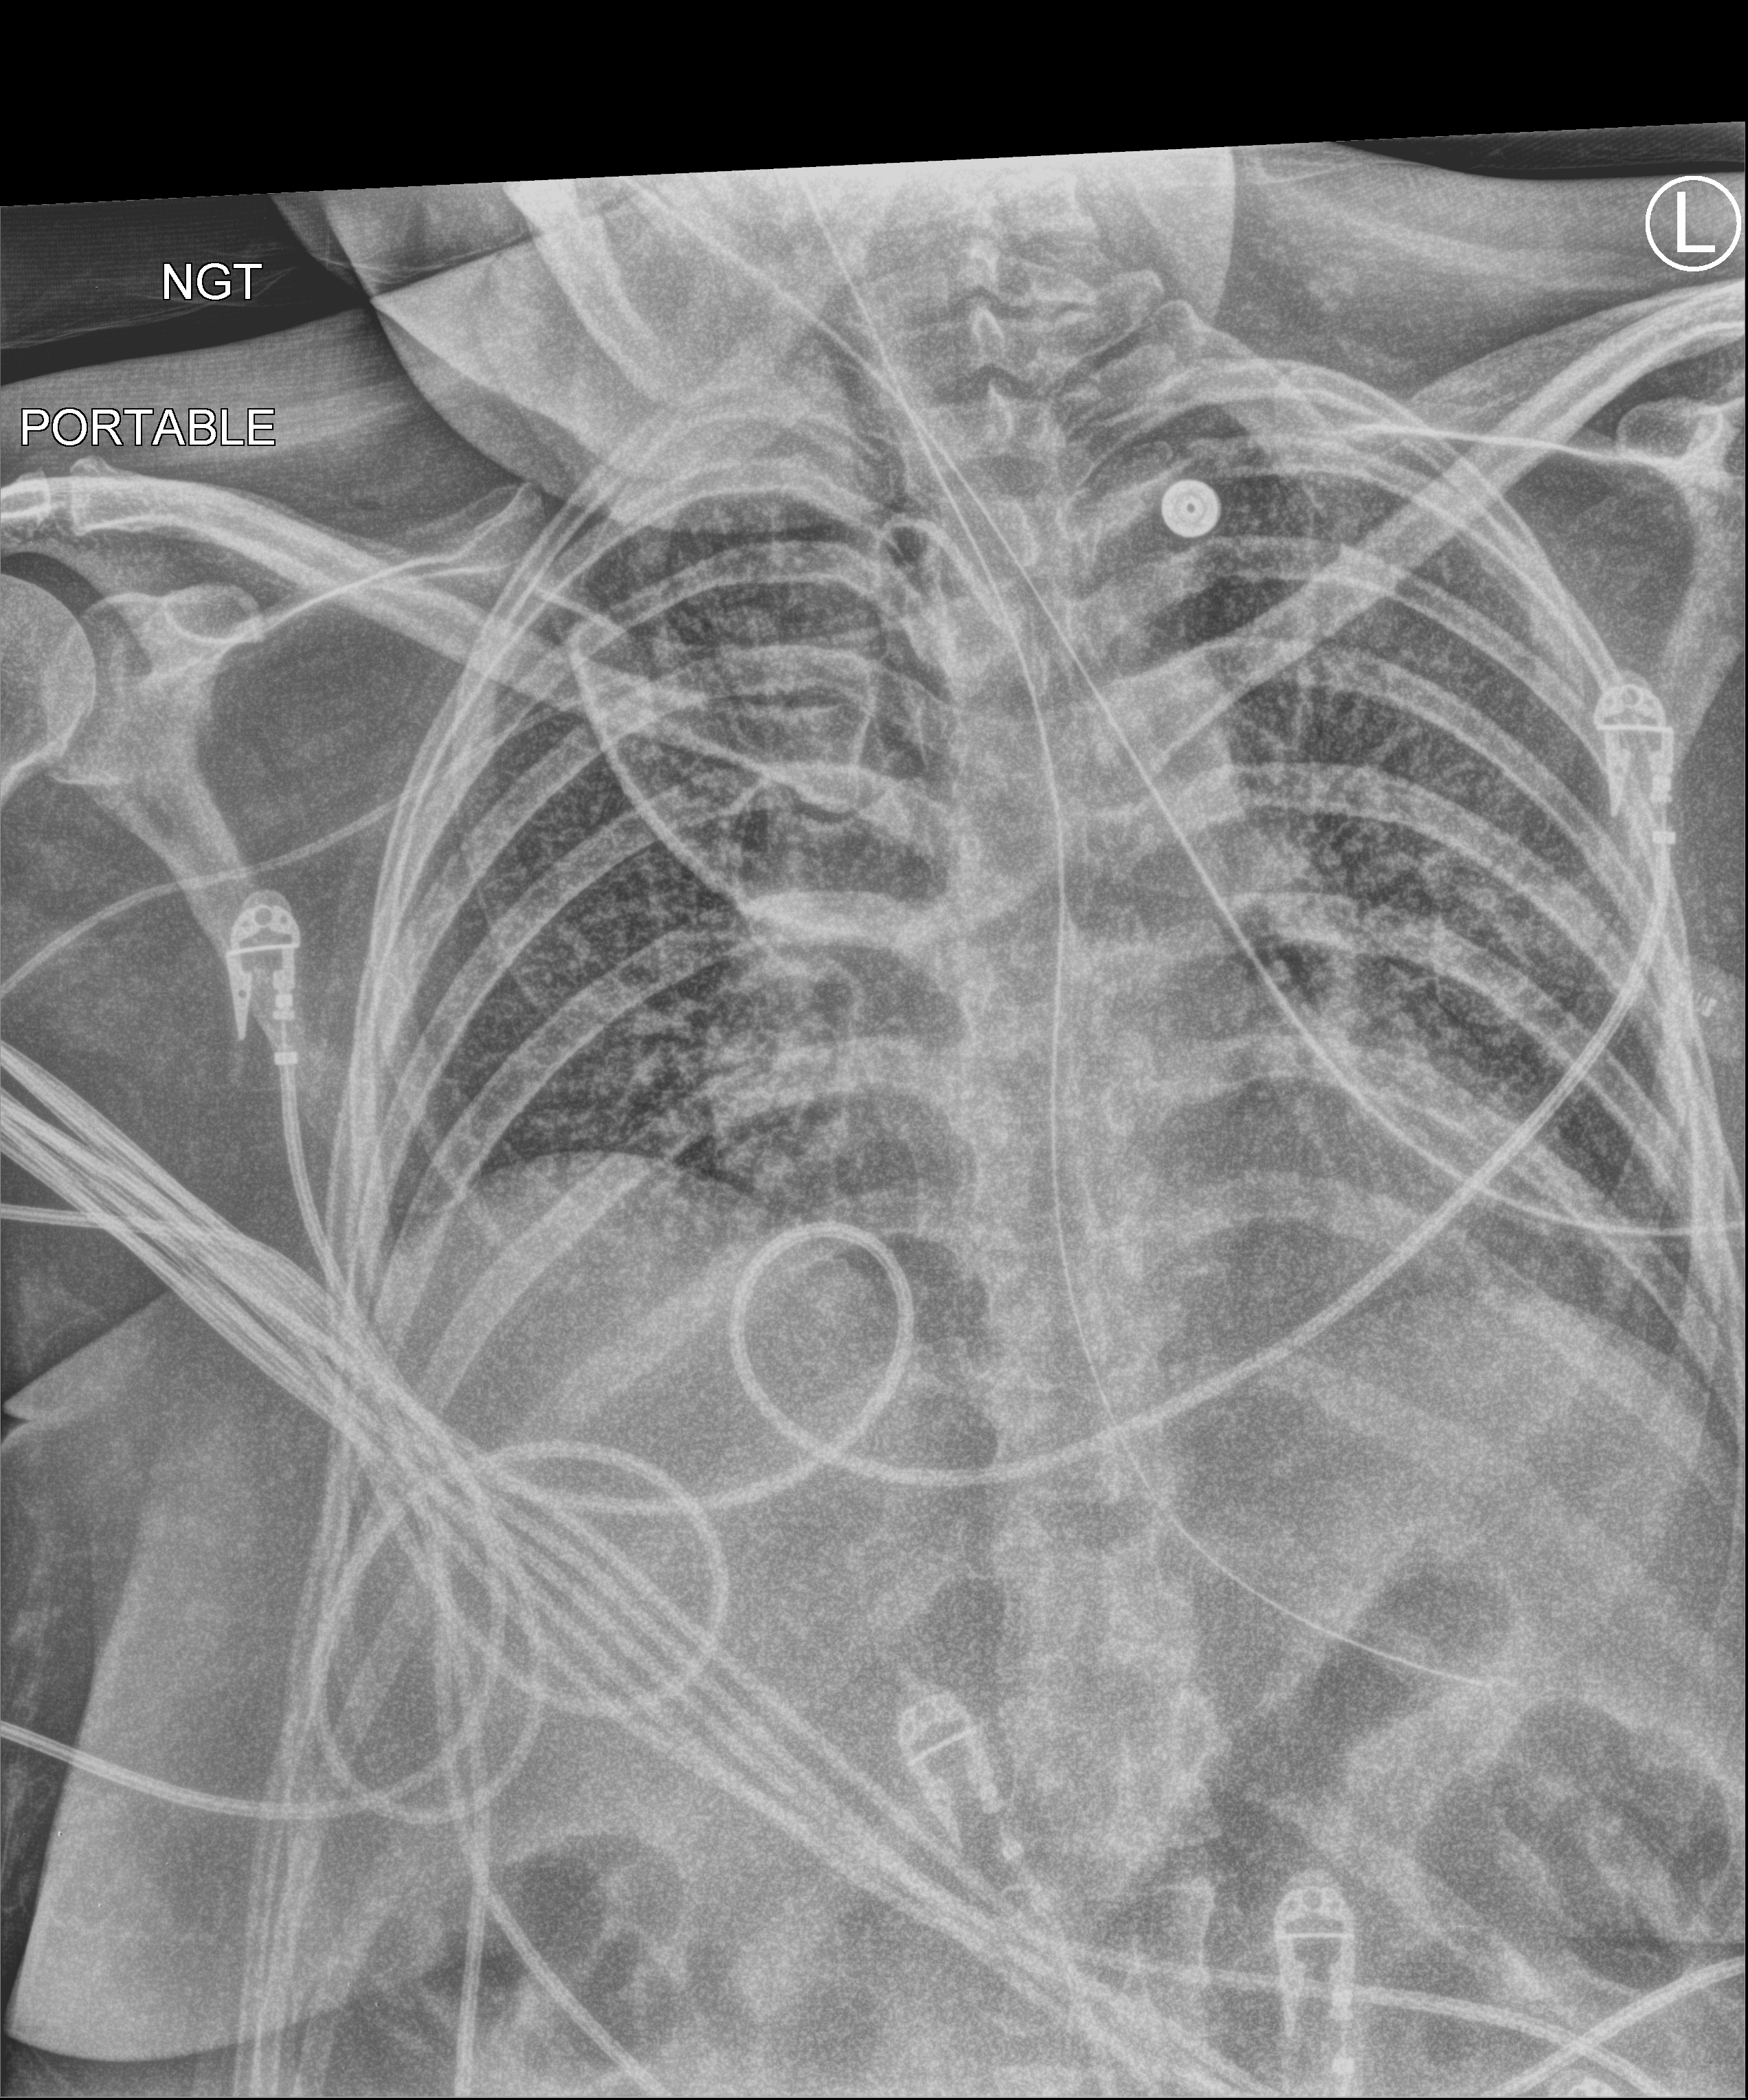
Bedside chest radiograph (computed radiography), anteroposterior (AP) projection. Patient hospitalised with COVID-19; female, aged 18–59 years.
From the hospital-stay record, not from the radiograph (when in the stay this image was taken is not recorded):
- mechanically ventilated during this hospital stay: yes
- hypertension (admission record): no
- length of hospital stay: 73 days